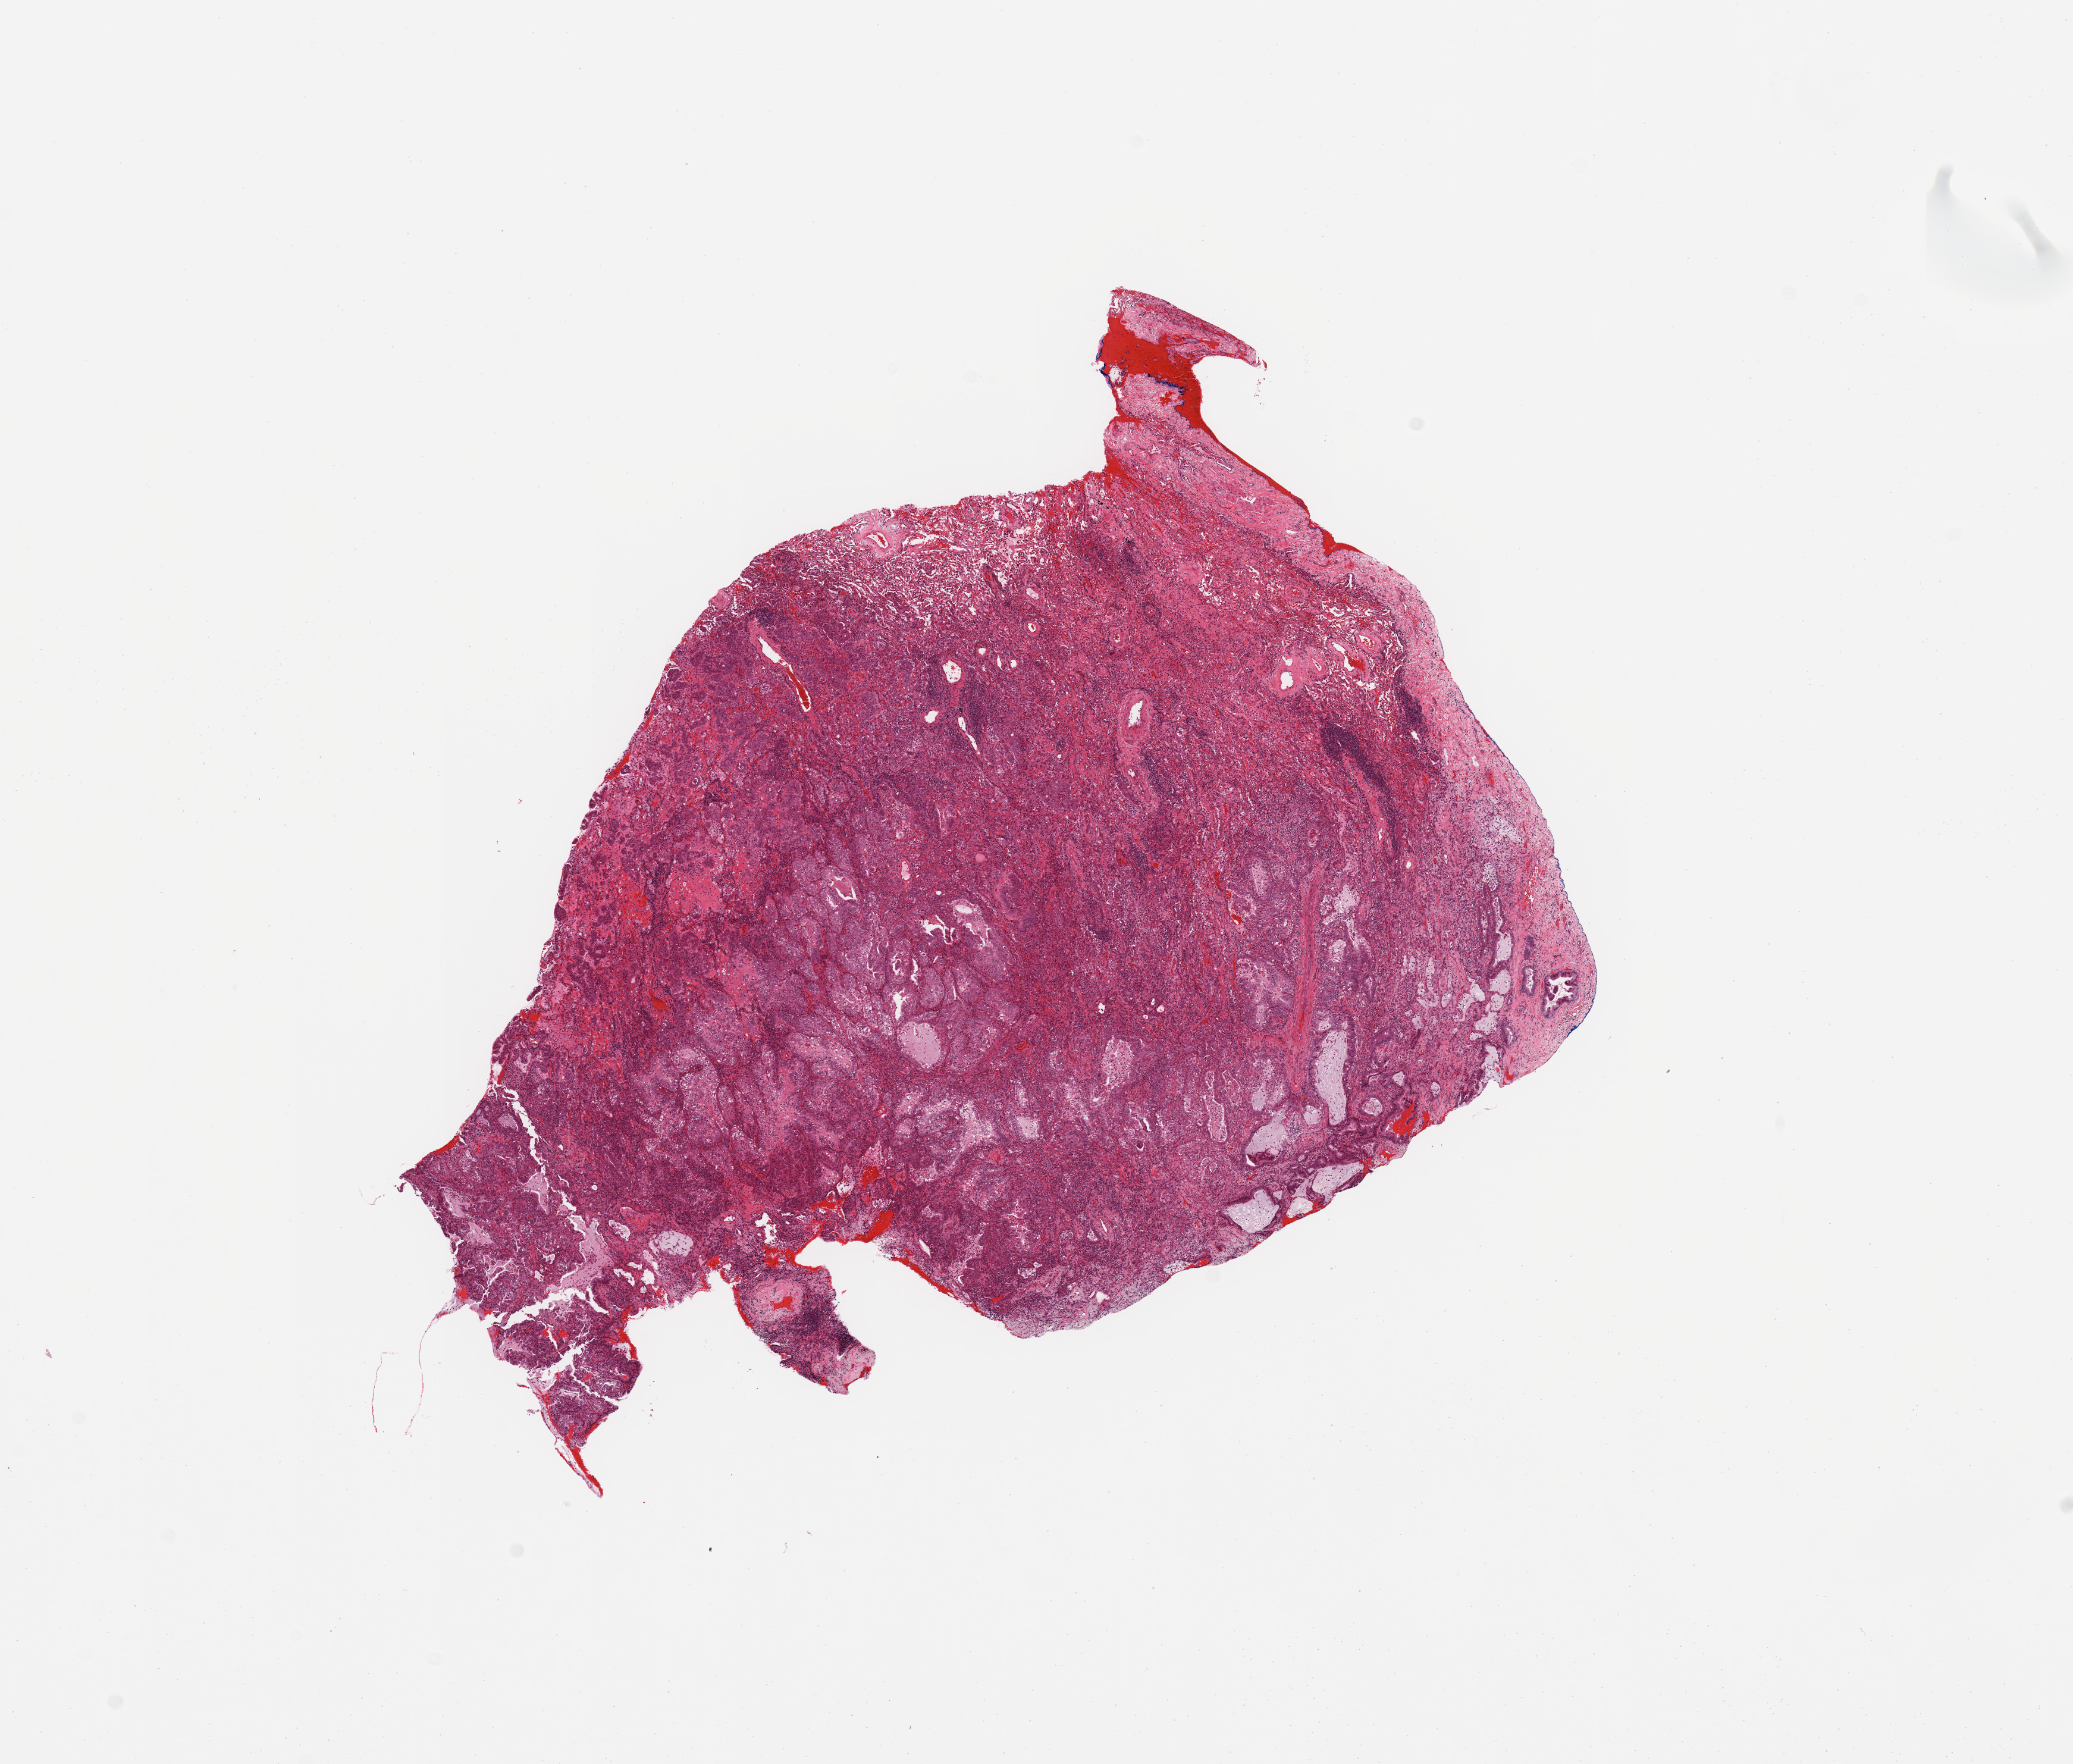
Digitized H&E tissue section (whole slide) — shown as a low-resolution overview of the whole scanned area (about 13.8 x 11.7 mm); tumour tissue sample, sampled site: lung. Male, 81 y/o.
Diagnosis: Adenocarcinoma, NOS.